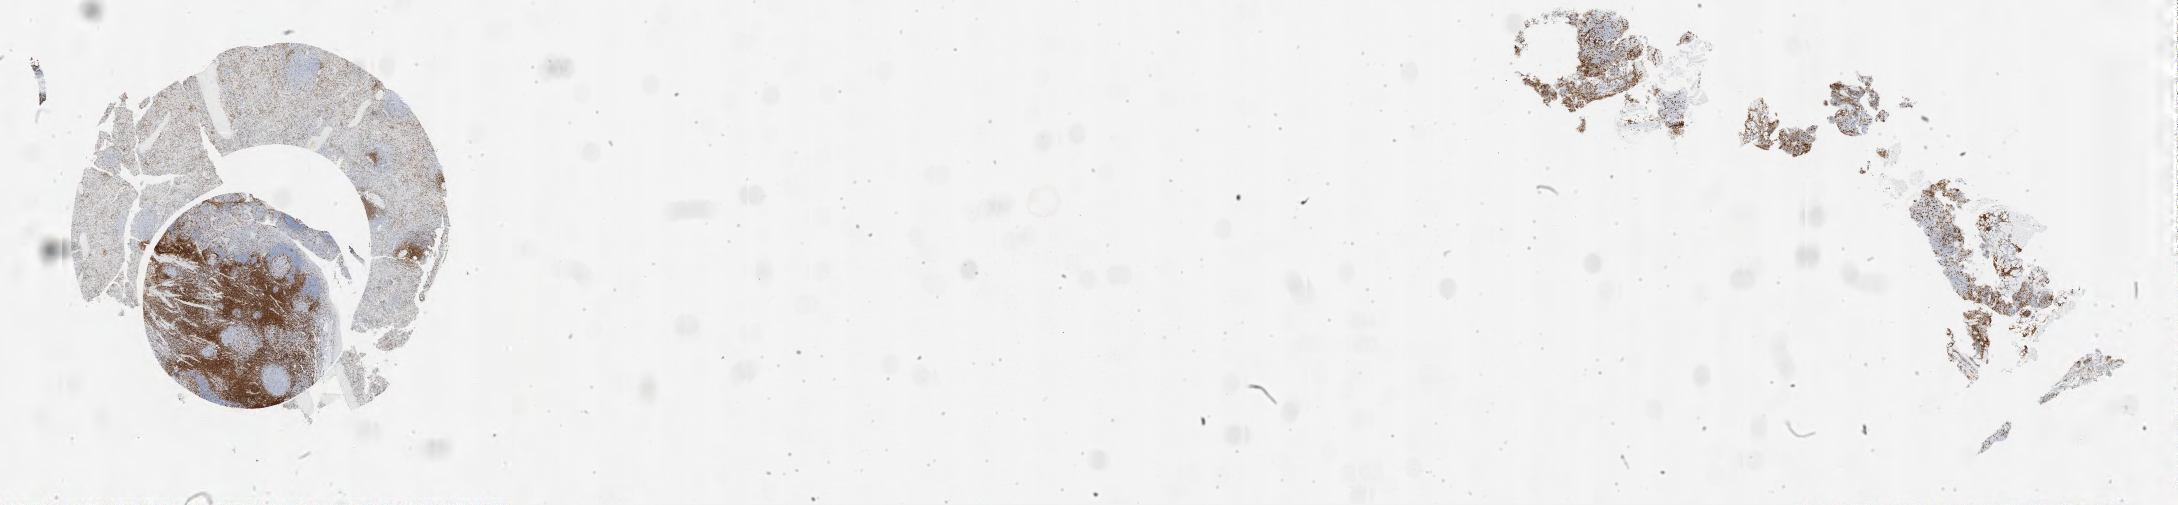
Whole-slide image, immunohistochemical stain for CD3 — shown as a low-resolution overview of the whole scanned area (about 35.0 x 8.1 mm). Tumor tissue. Patient: female, aged 69.
* histologic diagnosis: Burkitt lymphoma, NOS